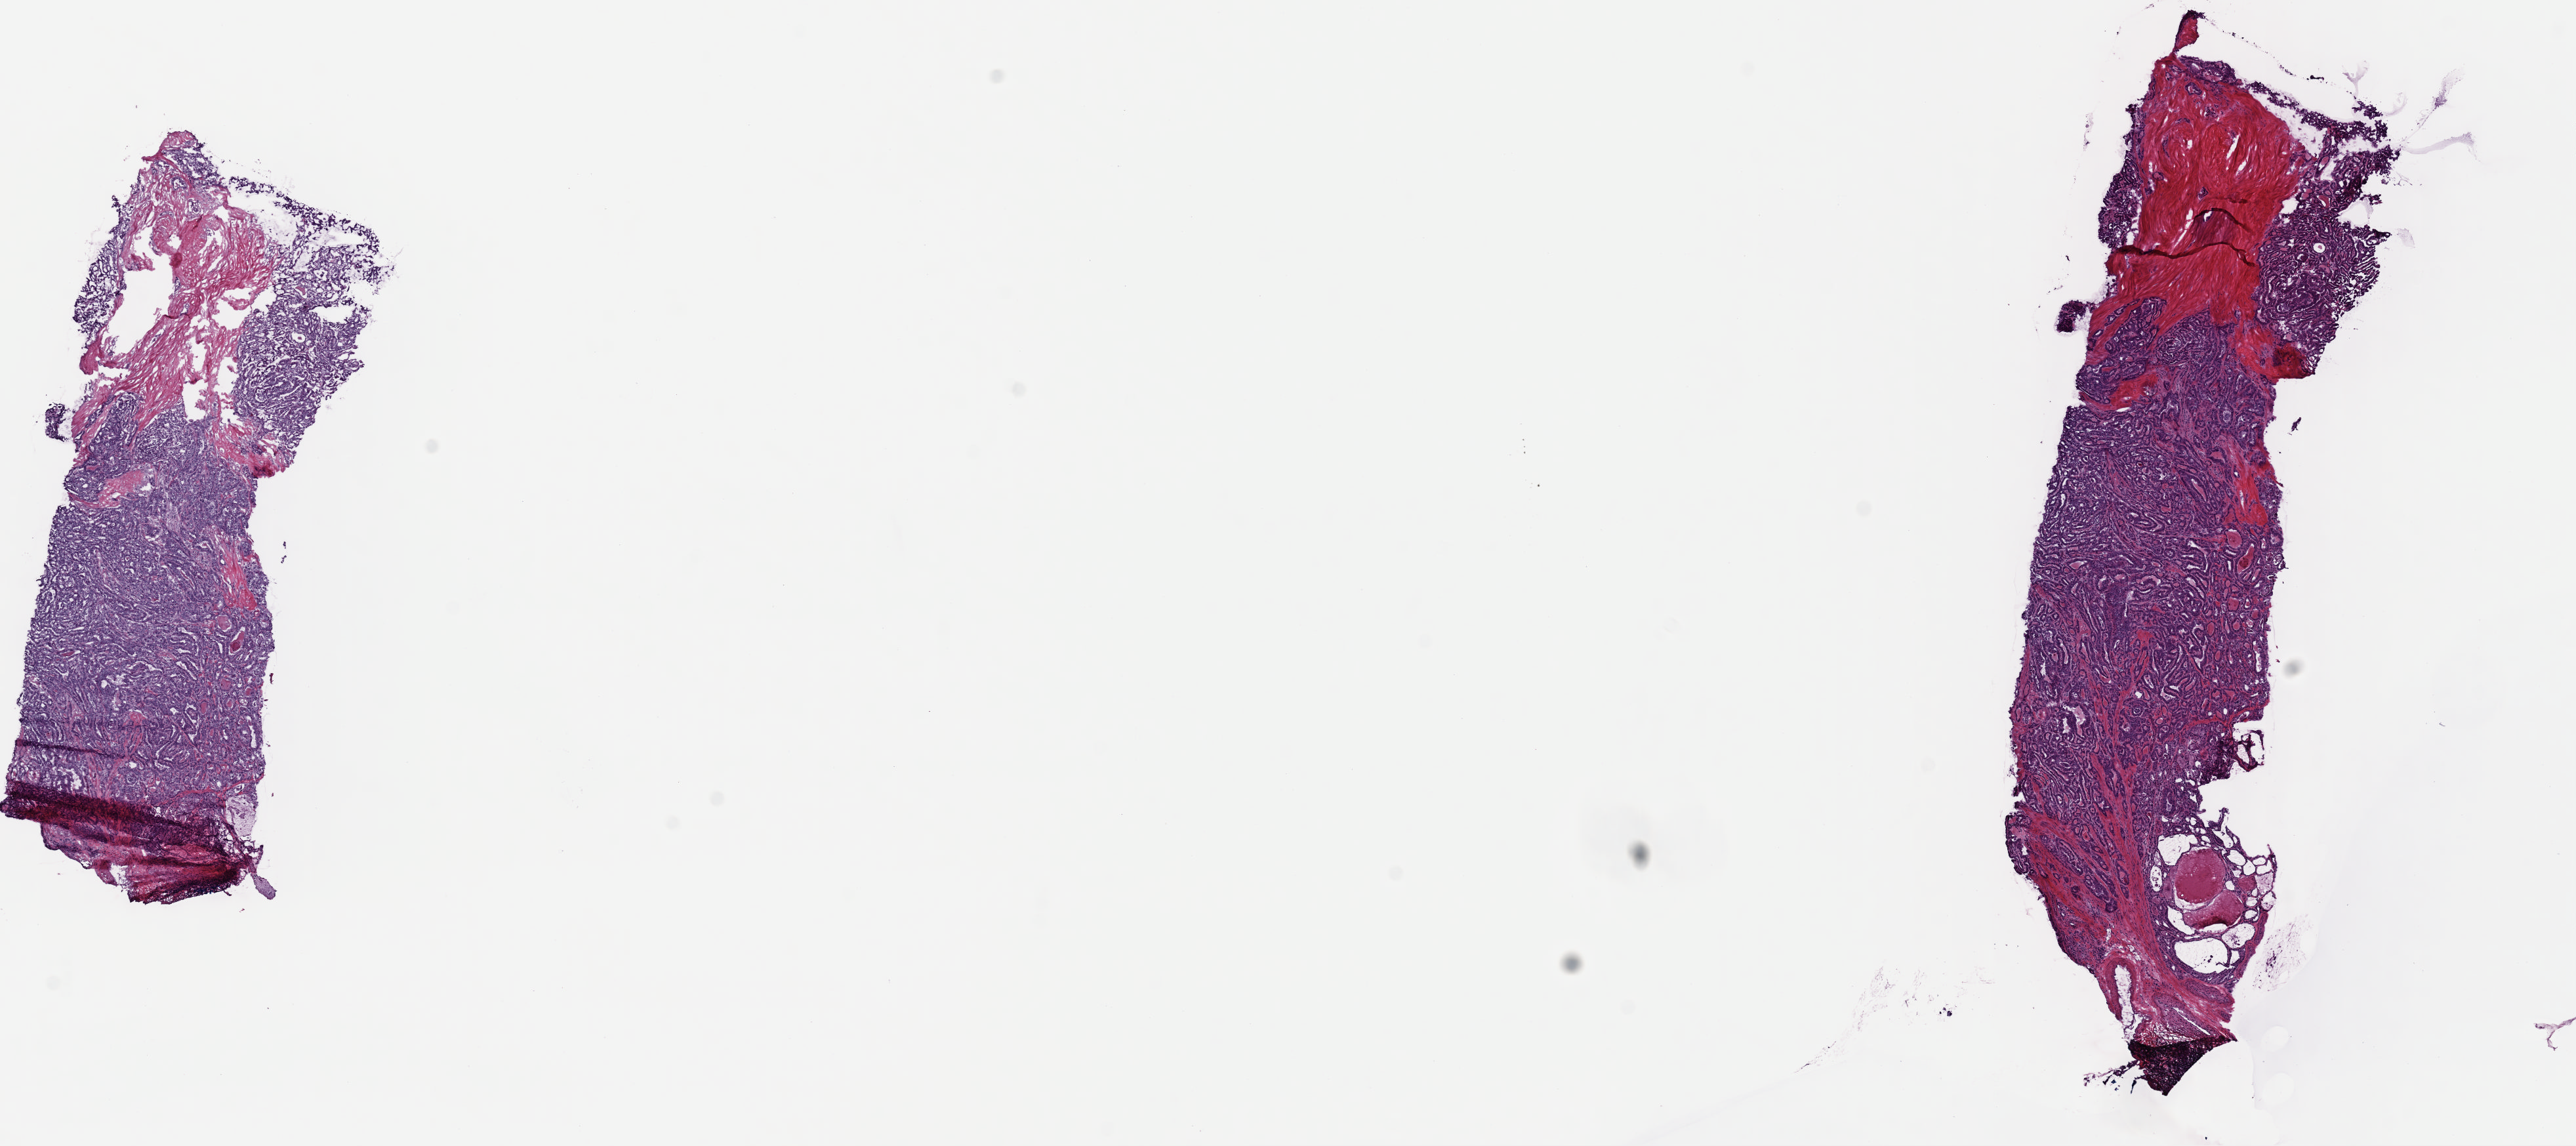
Whole-slide histology image, H&E, shown as a low-resolution overview of the whole scanned area (about 15.5 x 6.9 mm), frozen section, thyroid, primary tumour sample. Female patient; age at initial diagnosis 44 years. Pathologist review of this section (percent, as recorded): tumour cells 90%, tumour nuclei 93%, normal cells 0%, stromal cells 10%, necrosis 0%. Inflammatory infiltration, as recorded: lymphocyte infiltration 0%, monocyte infiltration 0%, neutrophil infiltration 0%.
Diagnosis: Papillary adenocarcinoma, NOS (thyroid gland). AJCC pathologic stage: I (6th edition).